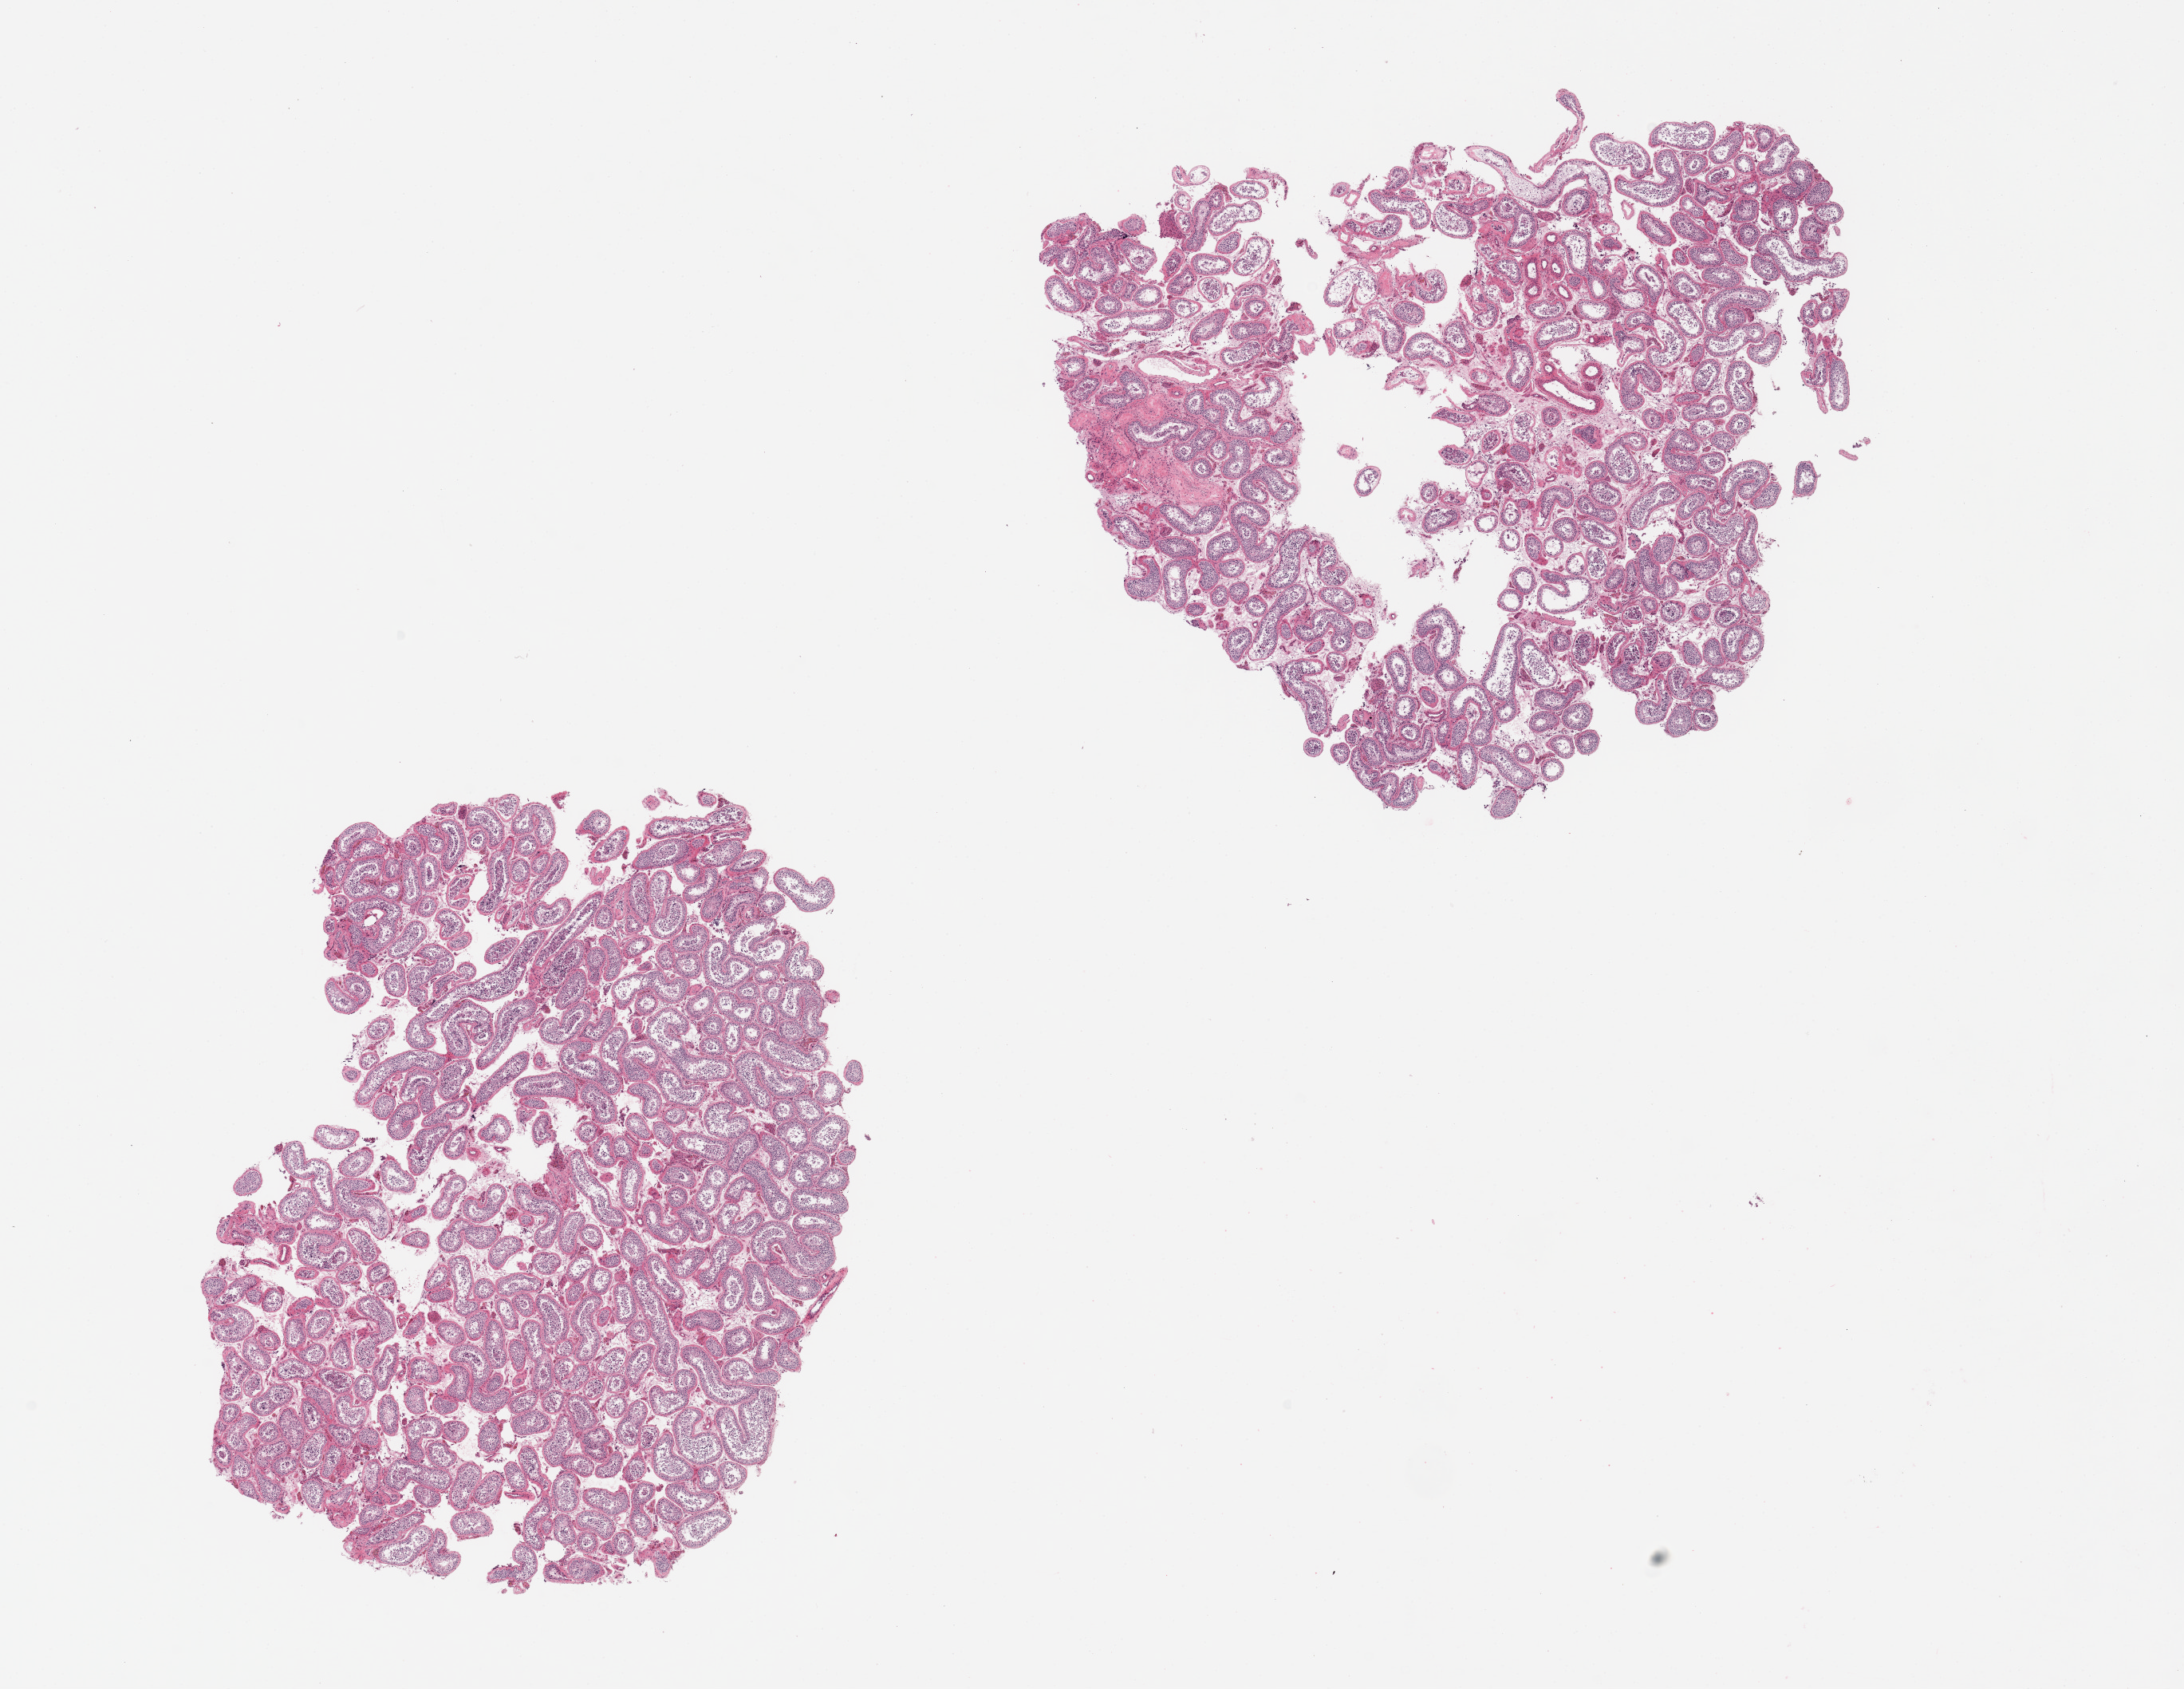
H&E whole-slide image — a low-resolution overview of the entire scanned area, about 21.7 x 16.7 mm. PAXgene-fixed, paraffin-embedded tissue. Sampled site (target tissue): testis. Donor tissue sample. Male donor.
* pathologist's review note for this sample: 2 pieces, active spermatogenesis